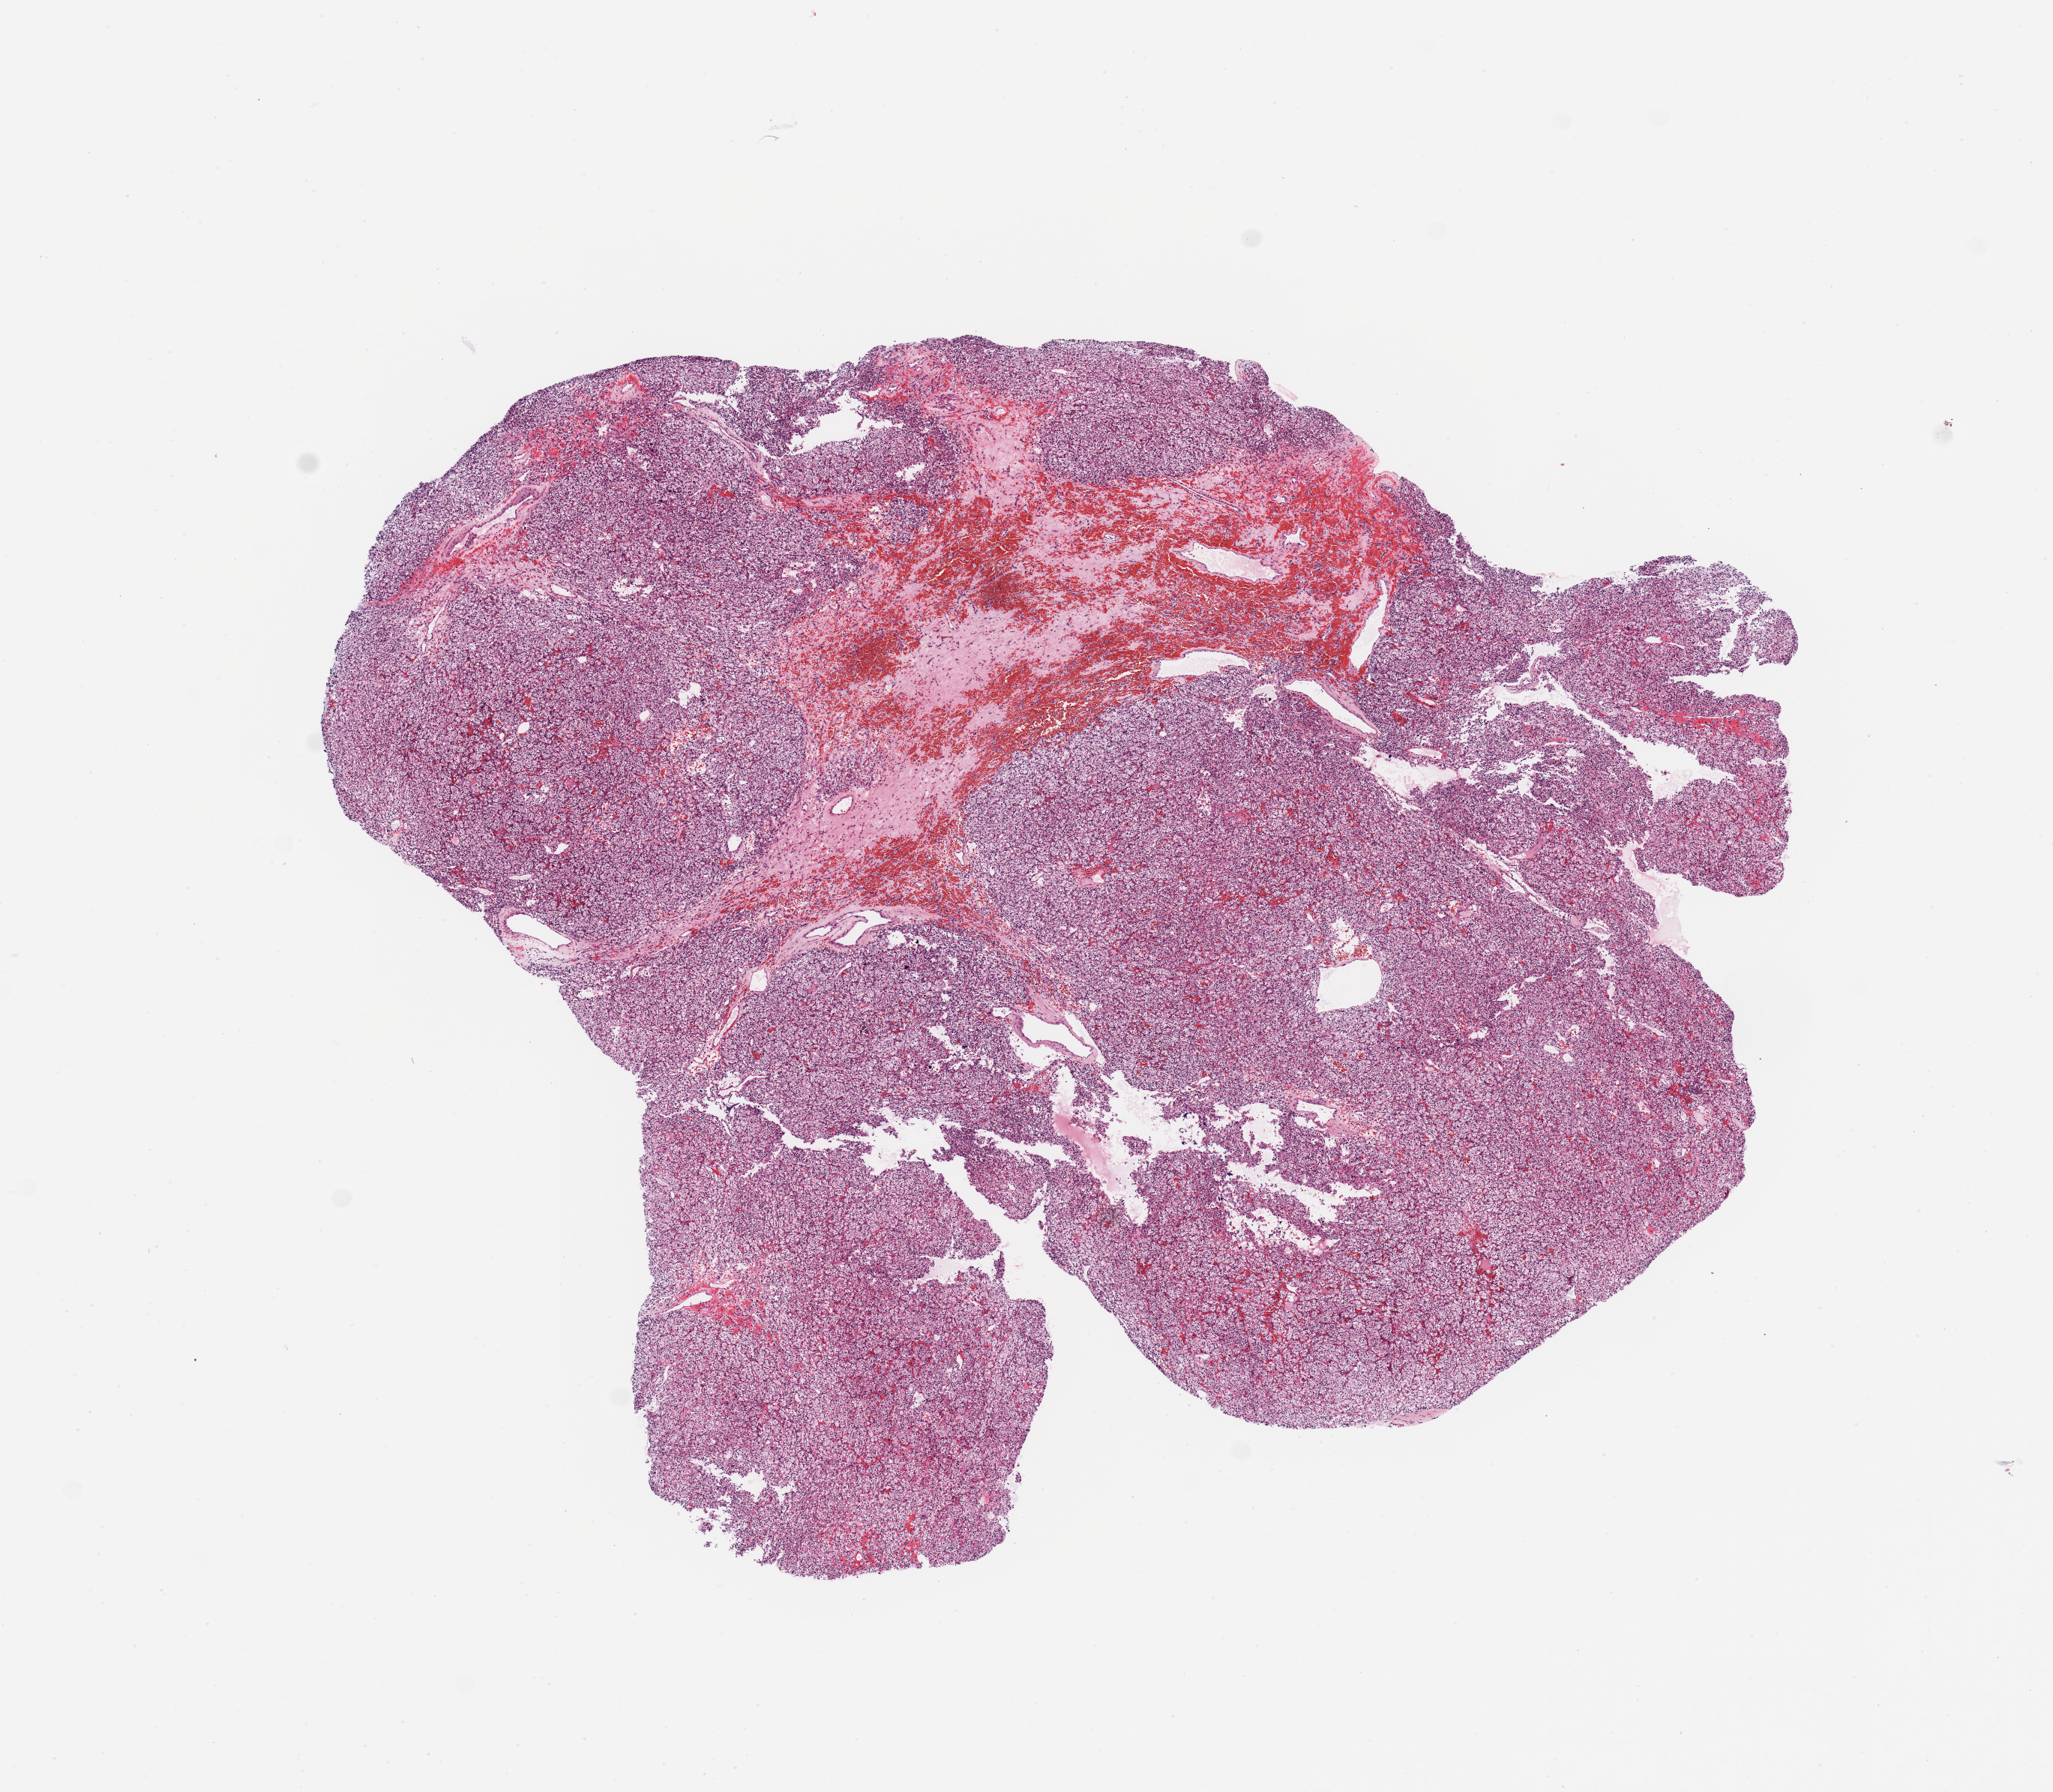
Digitized H&E tissue section (whole slide) — shown as a low-resolution overview of the whole scanned area (about 10.8 x 9.5 mm, from a 20x scan). Tumour tissue sample, sampled site: kidney. 66-year-old male patient. Pathologist review of this section (percent, as recorded): tumour nuclei 95%, necrosis 0%.
Histologic diagnosis: Renal cell carcinoma, NOS.